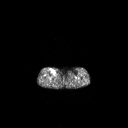
FDG PET of an extremity soft-tissue mass (from a PET/CT study), one axial slice. Slice 133 of 267 in the series (ordered by position). 3.27 mm slice thickness. 128 × 128 image matrix. Patient: female, 65 years. Case-level facts recorded for this patient, not image findings: histological type: undifferentiated – high grade; grade: high; site of the primary tumour: right thigh.
Annotated regions visible in this slice (expert contour drawn on MRI and transferred to this co-registered scan by the dataset authors):
- gross tumour volume (mass): box from (x=51, y=69) to (x=56, y=74) px